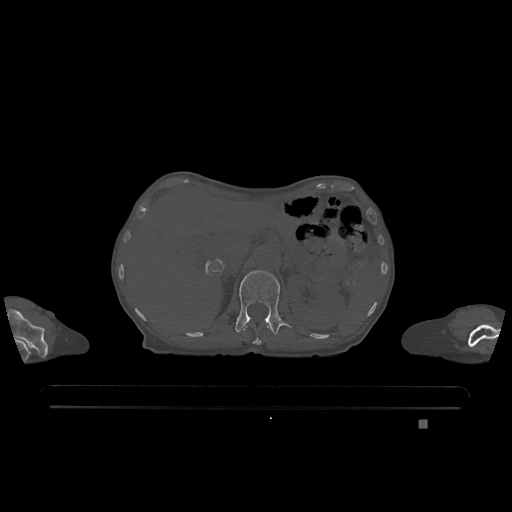
CT including the spine, one axial slice; position 487 of 1317 along the scan axis; bone window (W 1800 / L 400 HU); 0.5 mm slice thickness; 512 × 512 image matrix, field of view 500 × 500 mm. Female patient, age 74 years. Case-level facts recorded for this patient, not image findings: primary cancer: lung.
Structures marked on this image (semi-automatically segmented with operator editing):
- L1 vertebra: bounding box <235,270,292,335> (left, top, right, bottom; pixels)
- T12 vertebra: <243,326,268,345>